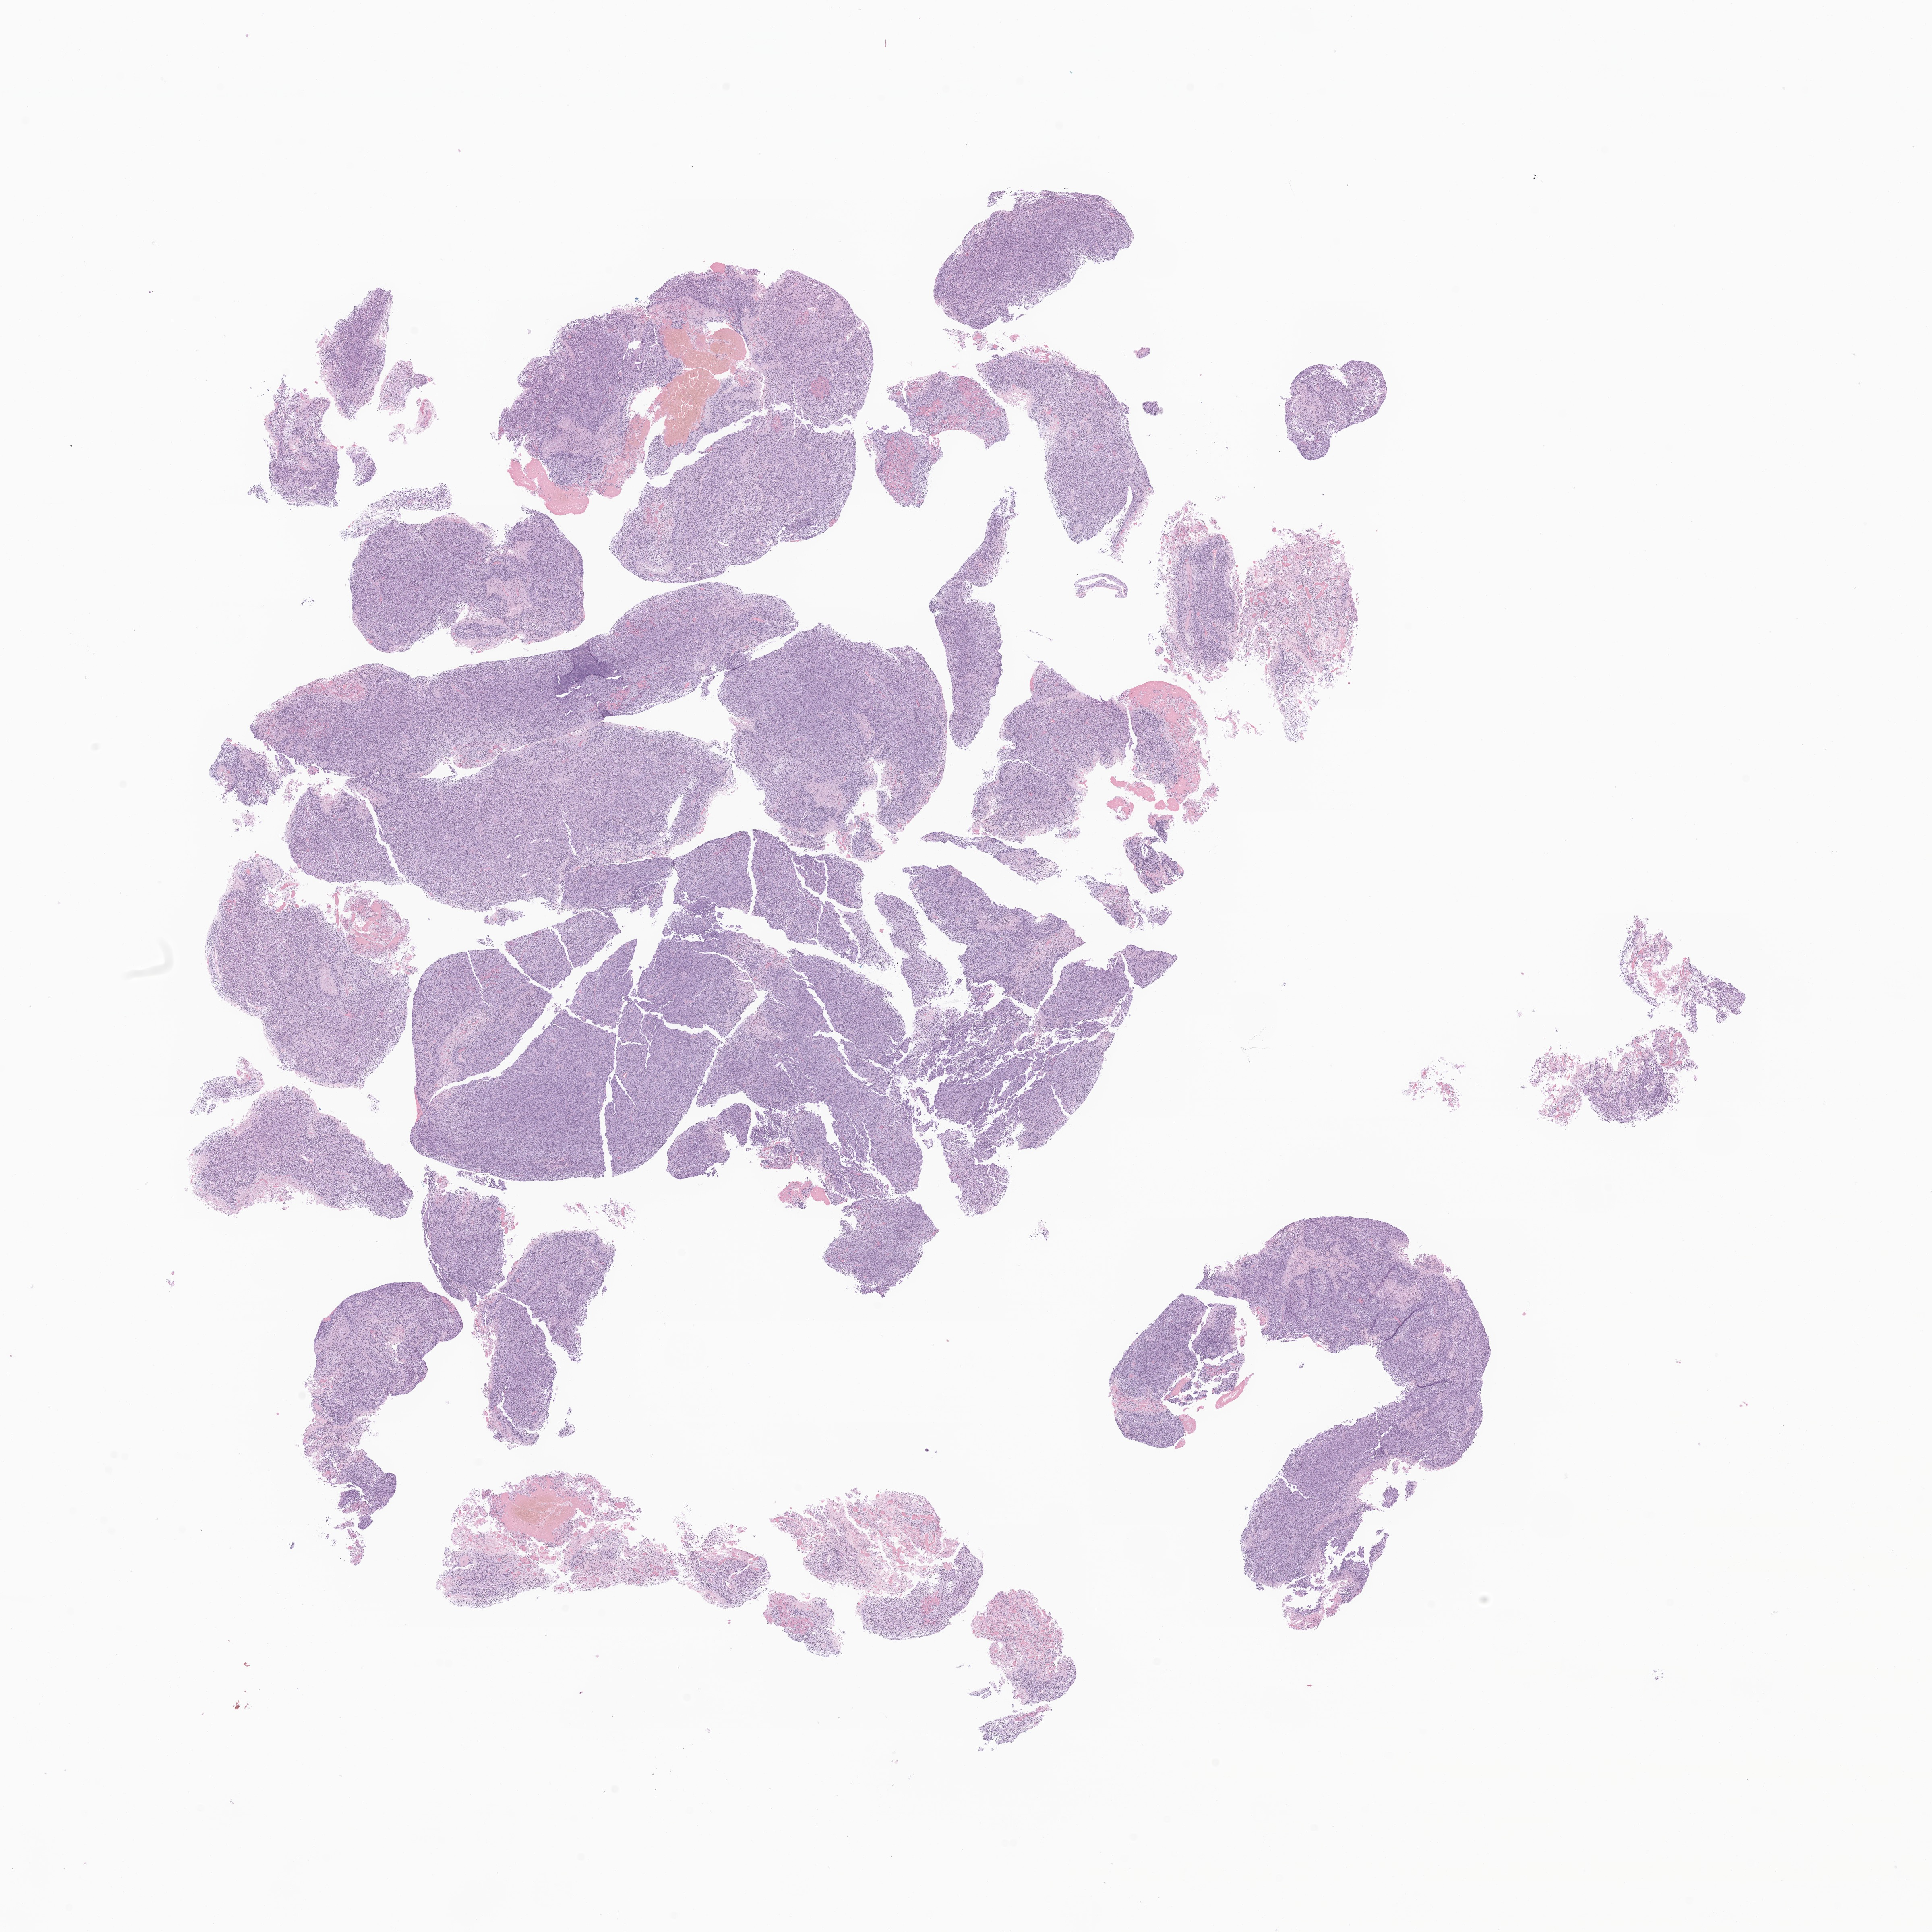
Digitized H&E-stained section of tumor tissue from the brain, low-resolution overview of the scanned area, about 20.2 x 20.2 mm. FFPE section. Patient male; age 69 months (5 years 9 months).
* diagnosis (ICD-O-3 morphology term): Astrocytoma, NOS